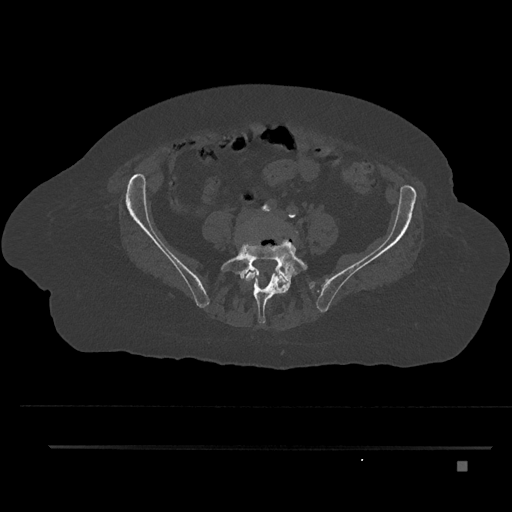
CT including the spine, one axial slice. Reconstruction kernel Br40s/3. Bone window (W 1800 / L 400 HU). 0.5 mm slice thickness. 512 × 512 image matrix, field of view 437 × 437 mm. Patient: female, 76 years. From the clinical record (not read from this slice): primary cancer: lung; vertebrae with lytic lesions (as recorded): T11, L3.
Outlined on this slice (semi-automatic segmentation, software-assisted and operator-edited):
- L4 vertebra: box from (x=240, y=230) to (x=298, y=303) px
- L5 vertebra: (x=220, y=240)–(x=308, y=324)